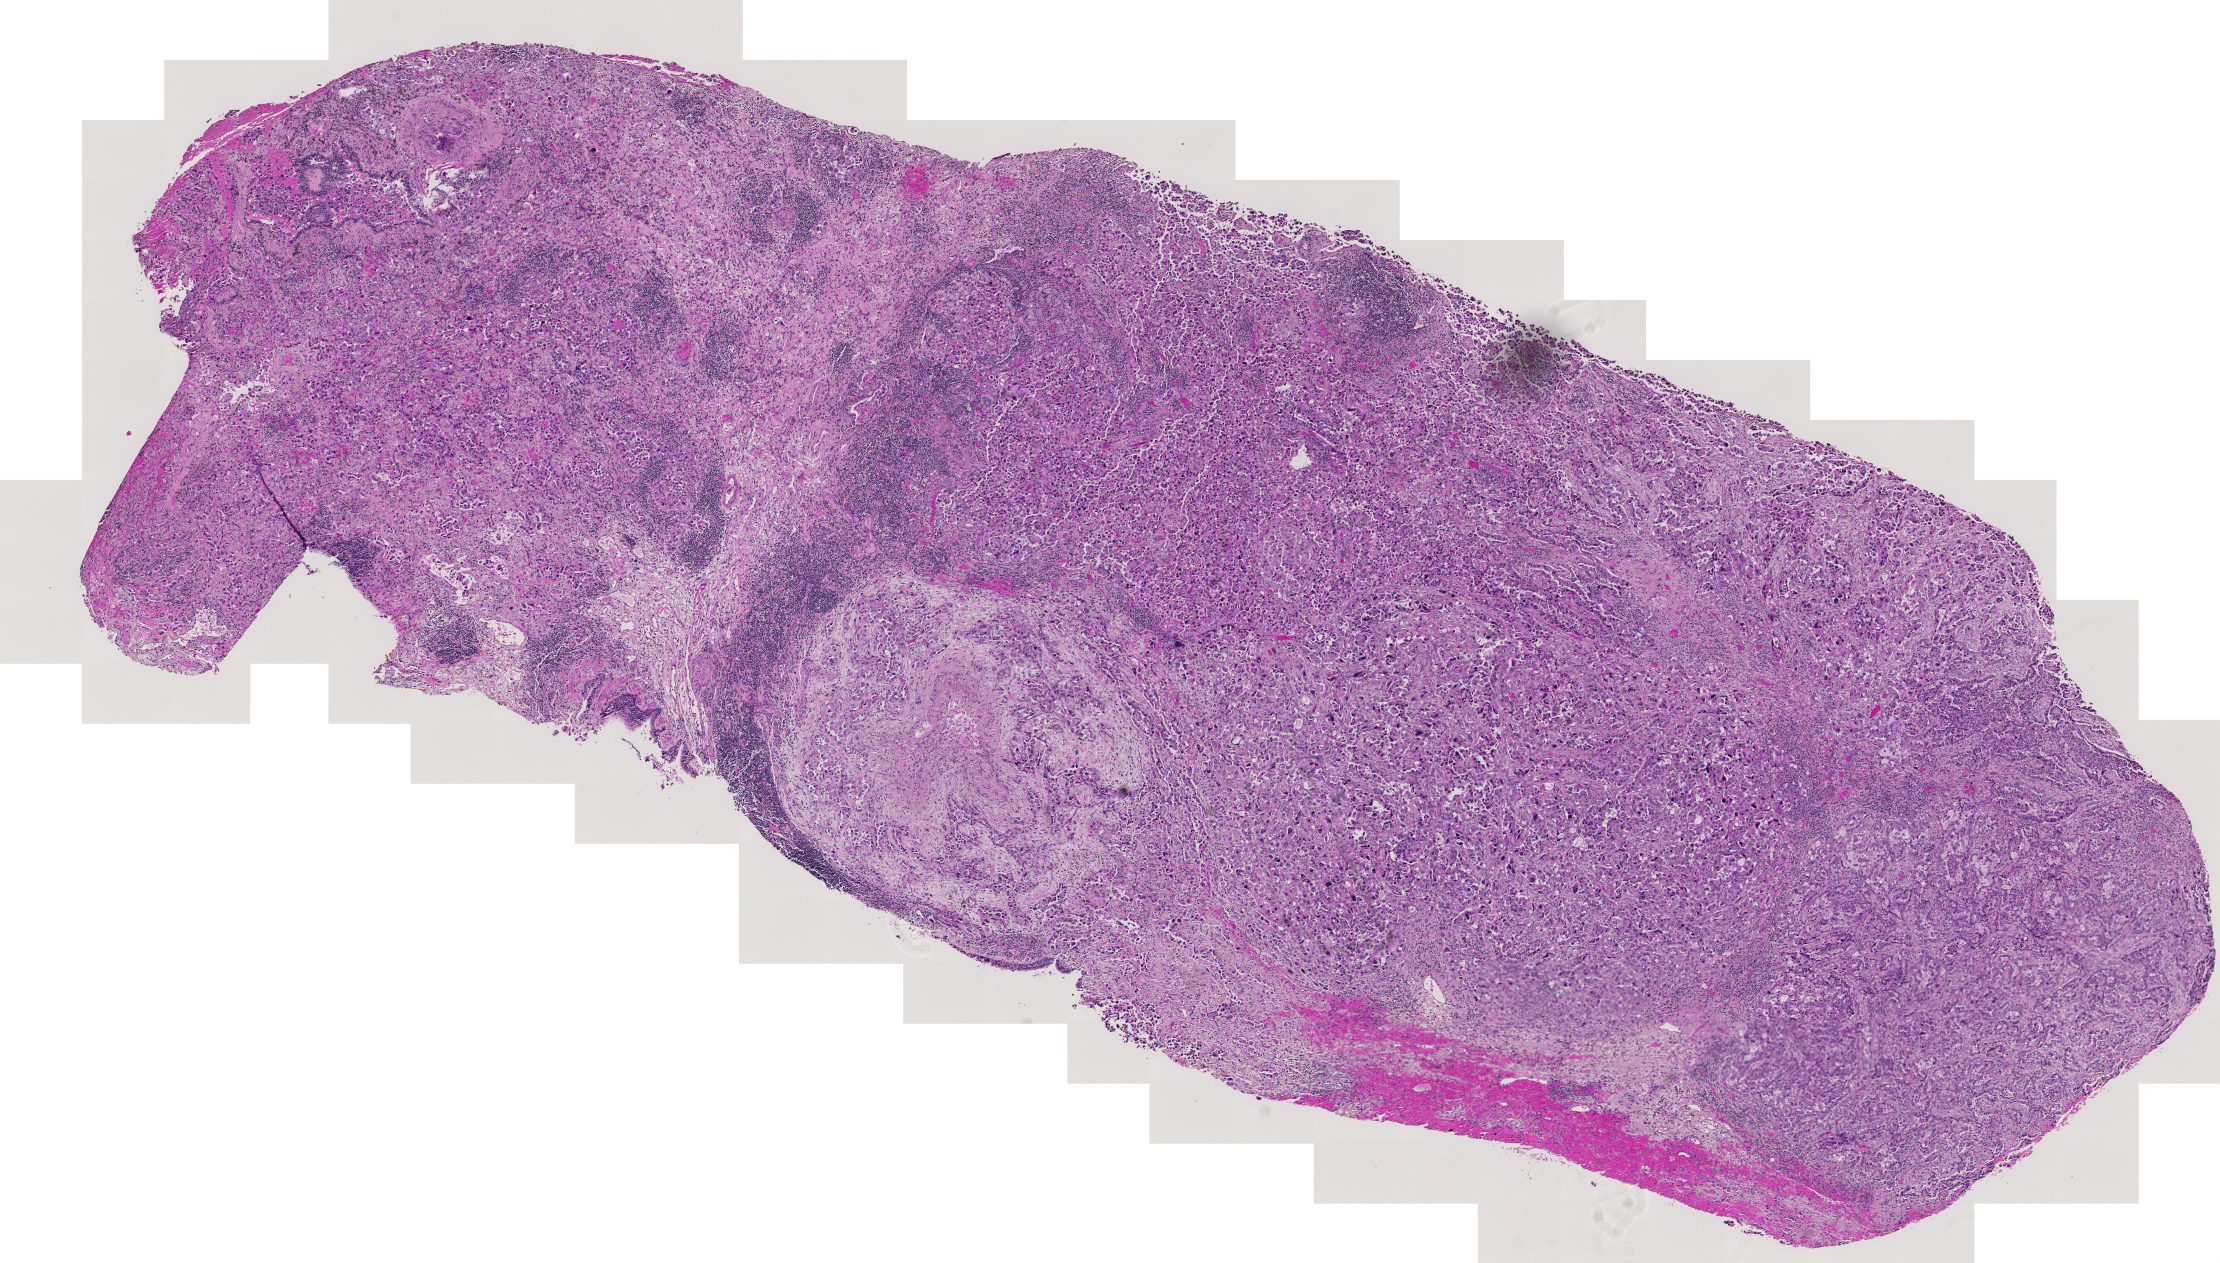
Hematoxylin and eosin (H&E) stained whole-slide image — low-resolution overview of the scanned area, about 11.5 x 6.5 mm. Tumour tissue sample, sampled site: lung. 68-year-old female patient. Histologic grade: G2 (moderately differentiated). Slide review estimates, as recorded: tumour nuclei 80%, necrosis 2%.
Diagnosis: Adenocarcinoma, NOS. AJCC pathologic stage: IIIA.